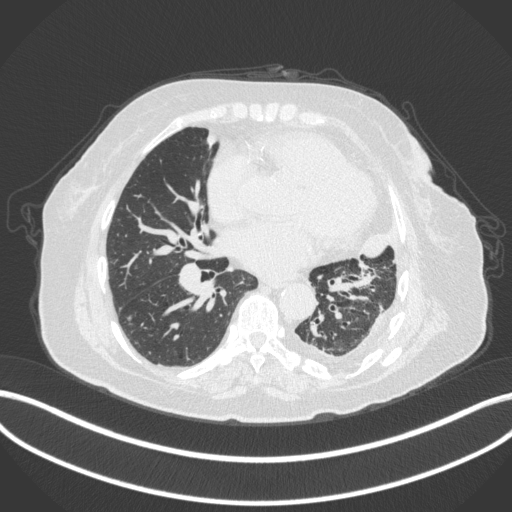
Chest CT, one axial slice; slice 165 of 399 in the series (ordered by position); reconstruction kernel B31f; lung window (W 1500 / L -600 HU); 1 mm slice thickness; 512 × 512 image matrix. Female patient, age 75 years. Case-level facts recorded for this patient, not image findings: clinical TNM (as recorded): T3 N3 M1.
Outlined on this slice (rectangle marked by the reading radiologist):
- lung tumour (recorded histology: adenocarcinoma): bounding box (x1, y1, x2, y2) in pixels: (361, 223, 390, 263)